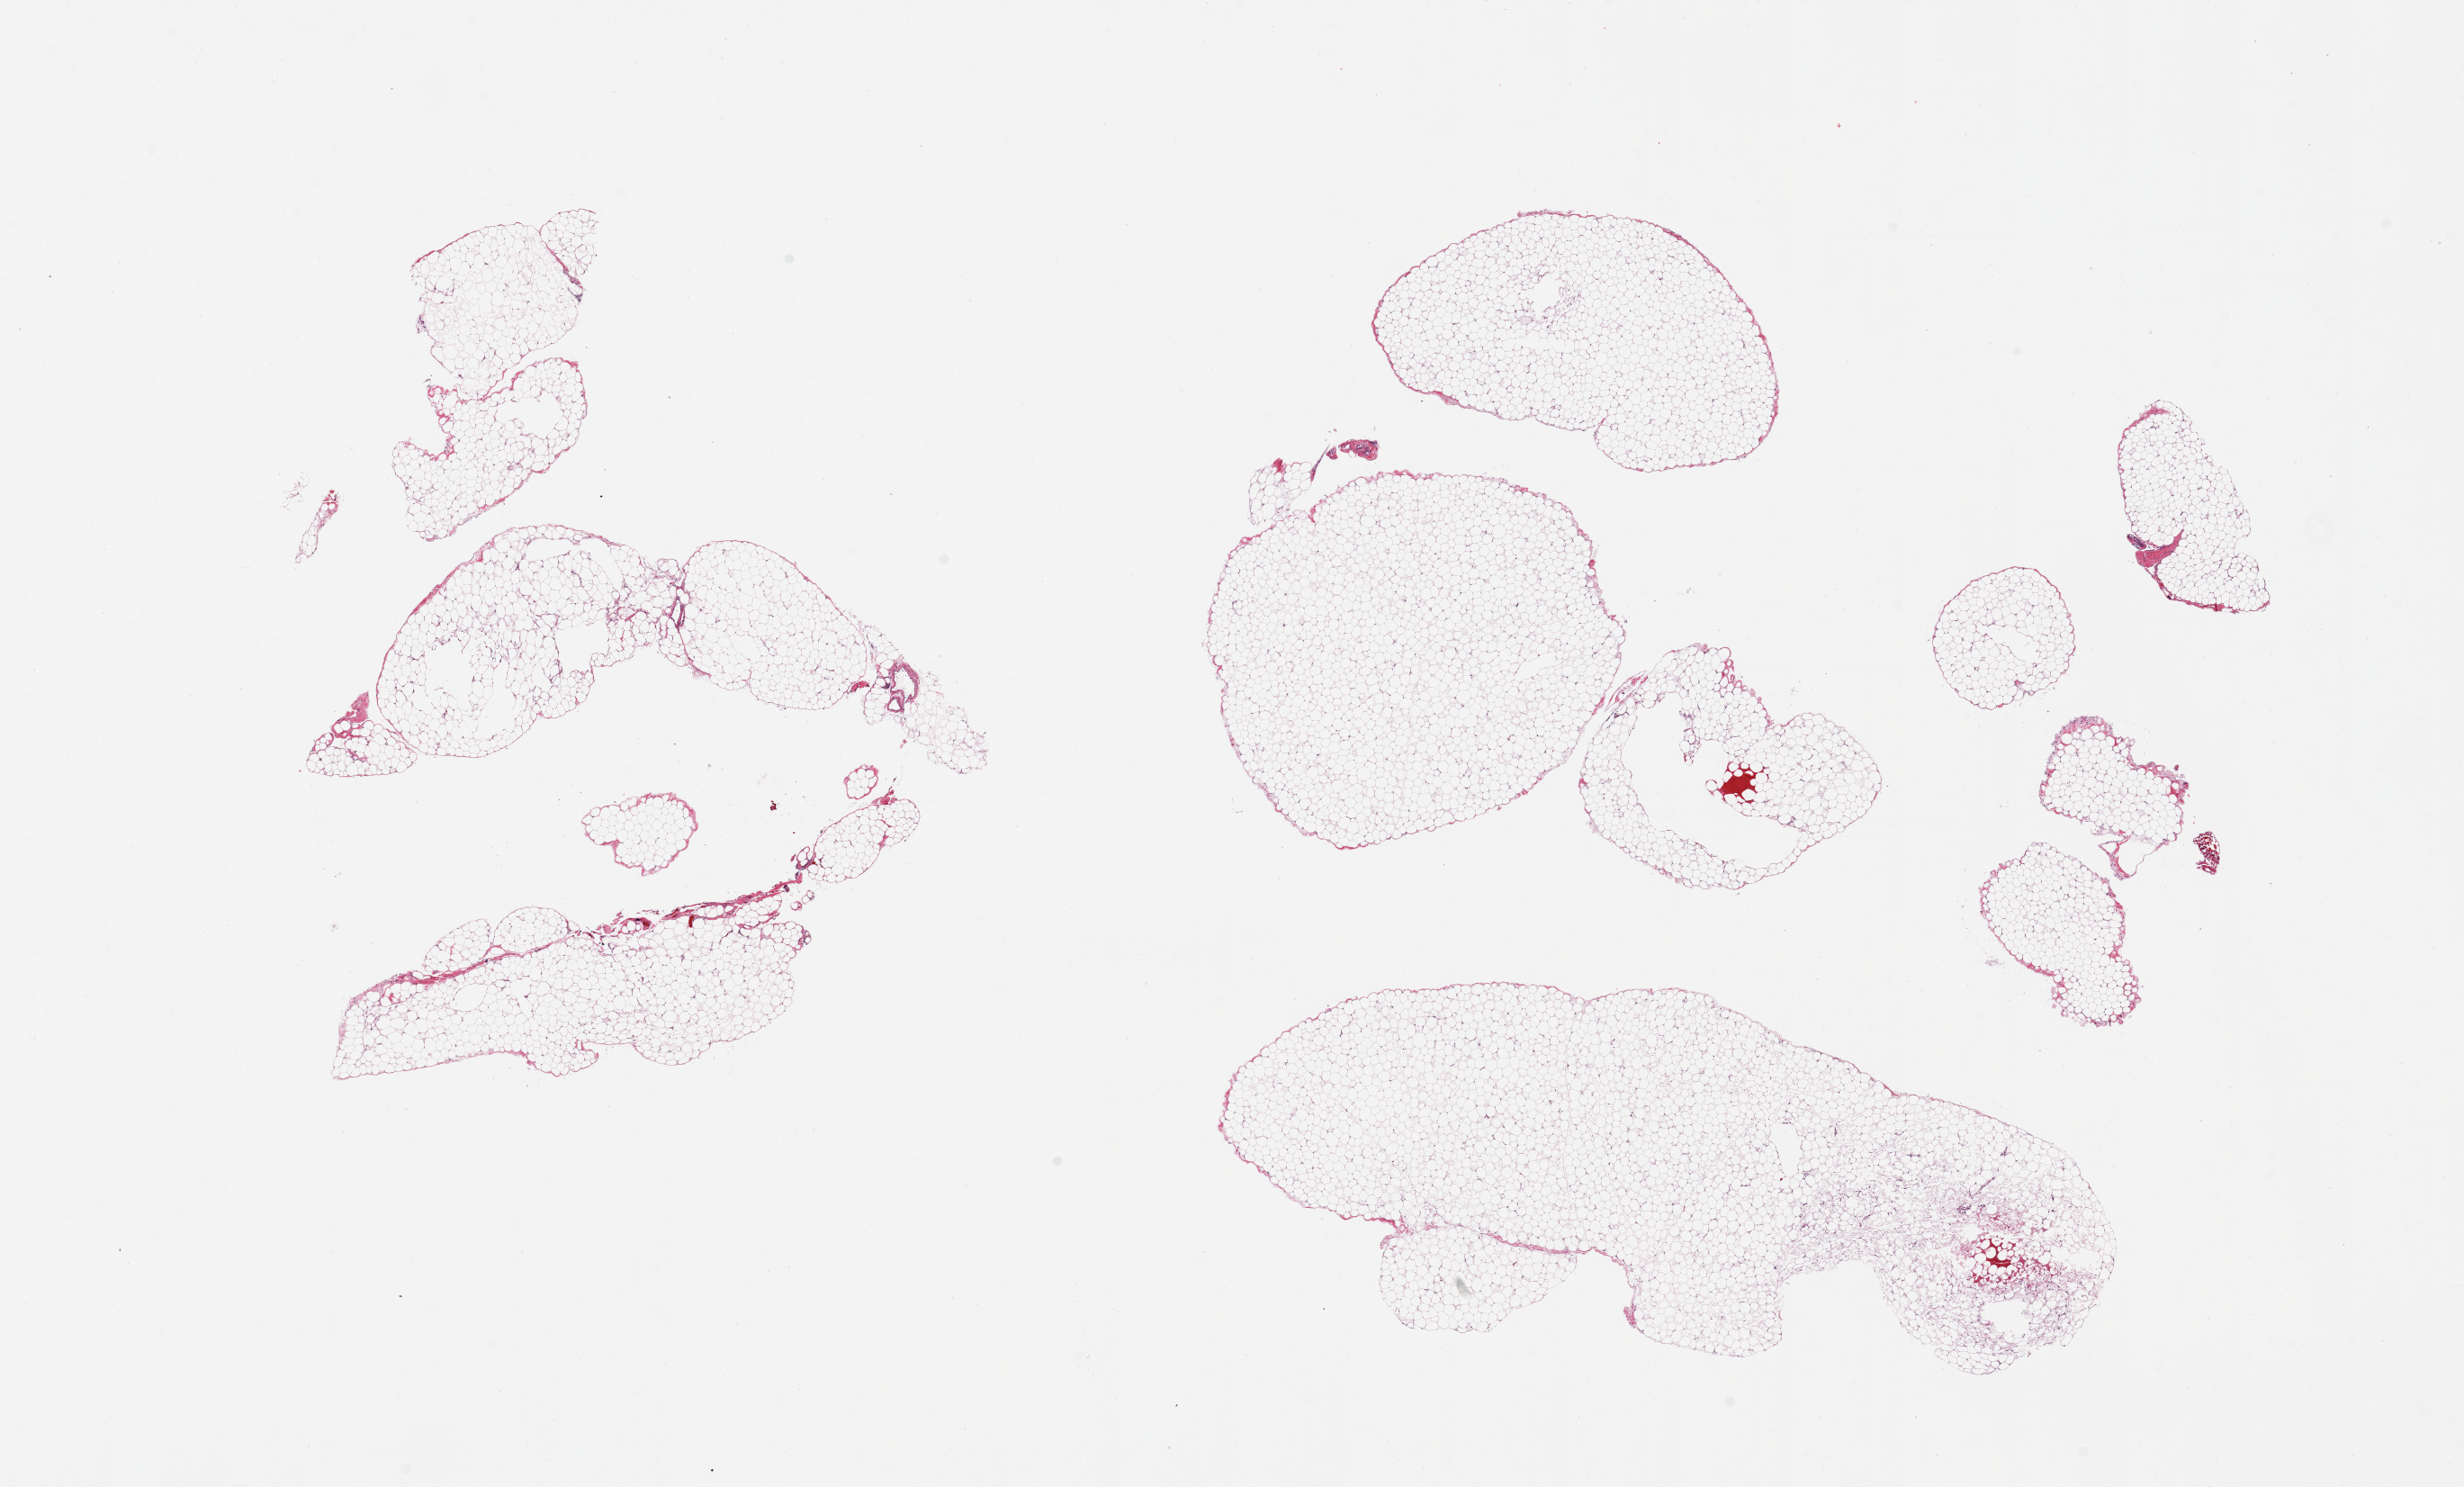
Whole-slide image, hematoxylin and eosin (H&E) stain, brightfield — low-resolution overview of the scanned area, about 21.7 x 13.1 mm (from a 20x scan), PAXgene-fixed paraffin-embedded (PFPE) section, section of omentum (target tissue), tissue donor sample. Donor sex: female.
Reviewer comment on this tissue sample: 2 pieces.